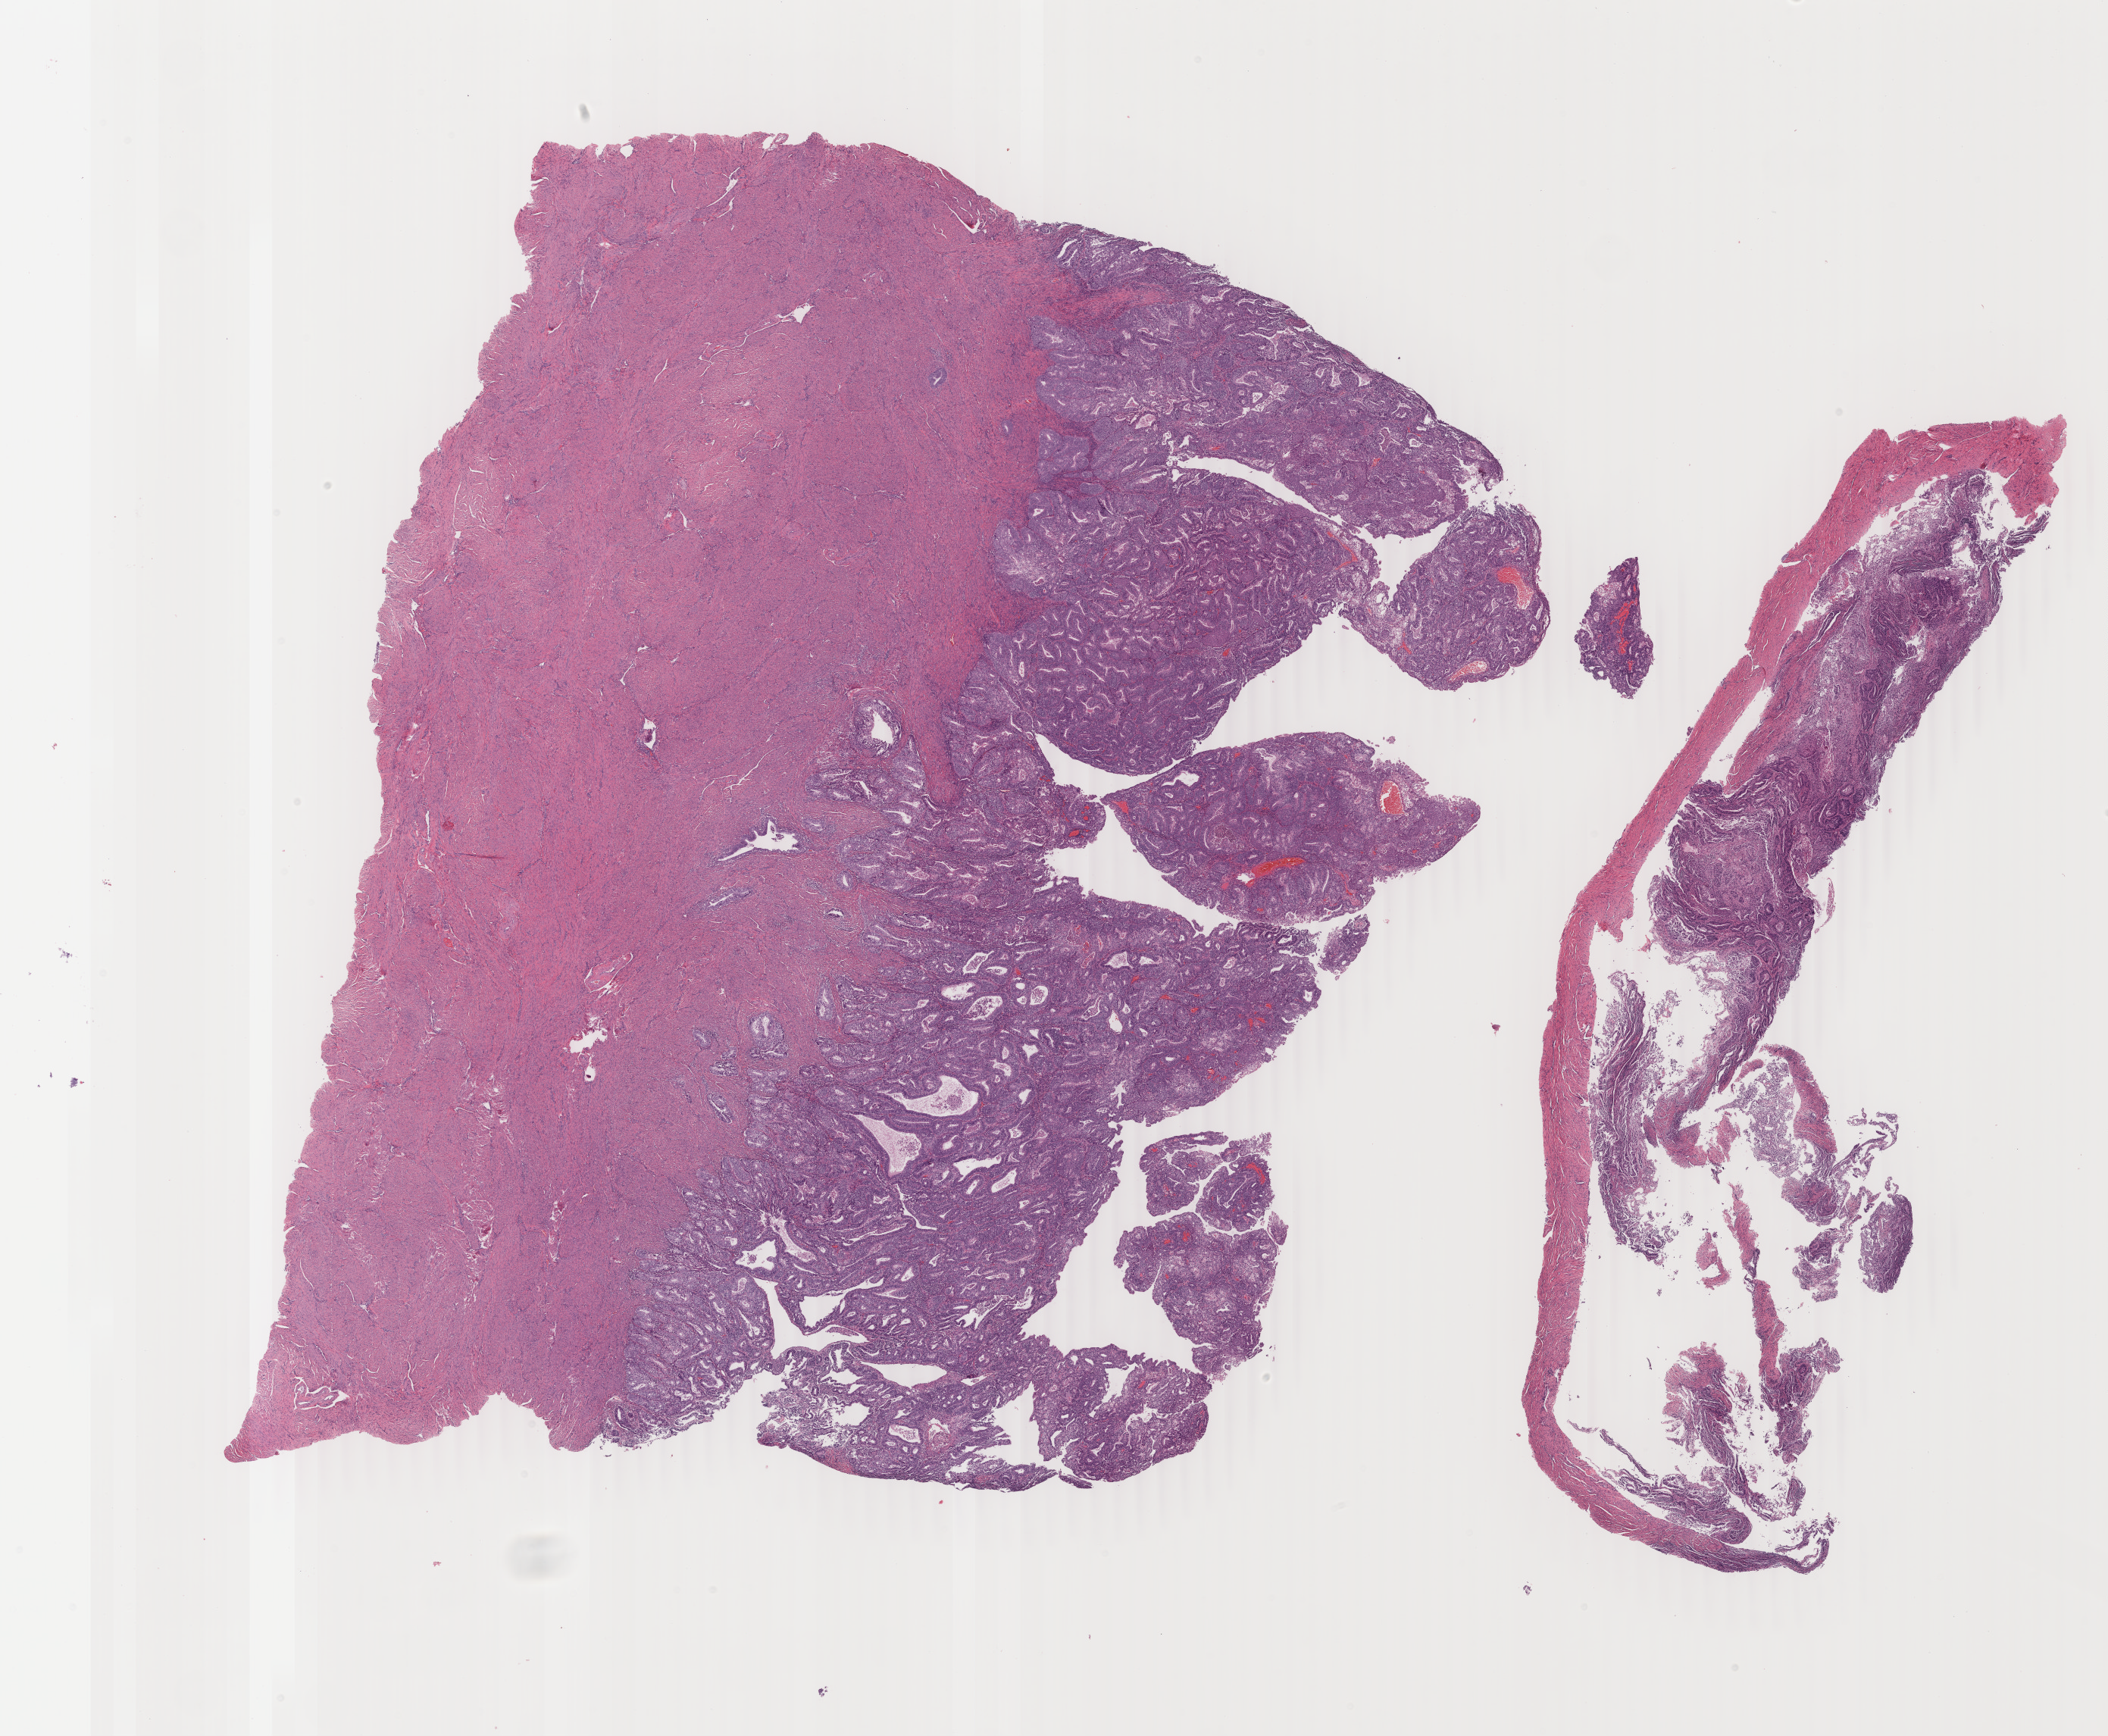
Whole-slide histology image, Hematoxylin and eosin (H&E) stained, whole scanned area (about 22.1 x 18.2 mm, acquisition: 40x scan) shown as a low-resolution overview. FFPE section. Uterus, primary tumour sample. Female, age 54 years at initial diagnosis. Histologic grade: G2 (moderately differentiated).
• histologic diagnosis: Endometrioid adenocarcinoma, NOS (endometrium)
• FIGO stage: II